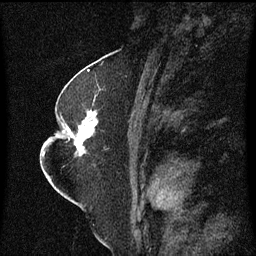
Breast MRI (dynamic contrast-enhanced), one sagittal slice; slice 33 of 60 in the series (ordered by position); dynamic contrast-enhanced series, image 2 of 3 at this slice position (ordered by acquisition); 1.5 T; TE 4.2 ms, TR 8.4 ms; 2 mm slice thickness; 256 × 256 image matrix. Patient: female, 52 years. Case-level facts recorded for this patient, not image findings: setting: breast cancer imaged before/during neoadjuvant chemotherapy; receptor status: HR-positive, HER2-negative.
Structures marked on this image (semi-automatic segmentation, software-assisted and operator-edited):
- analysis volume of interest (the breast-tissue region the enhancement analysis was run in; not a lesion): bounding box (x1, y1, x2, y2) in pixels: (64, 110, 109, 167)
- tumour enhancement mask (voxels above the 70 % enhancement threshold inside the analysis volume of interest): (72, 112, 99, 157)